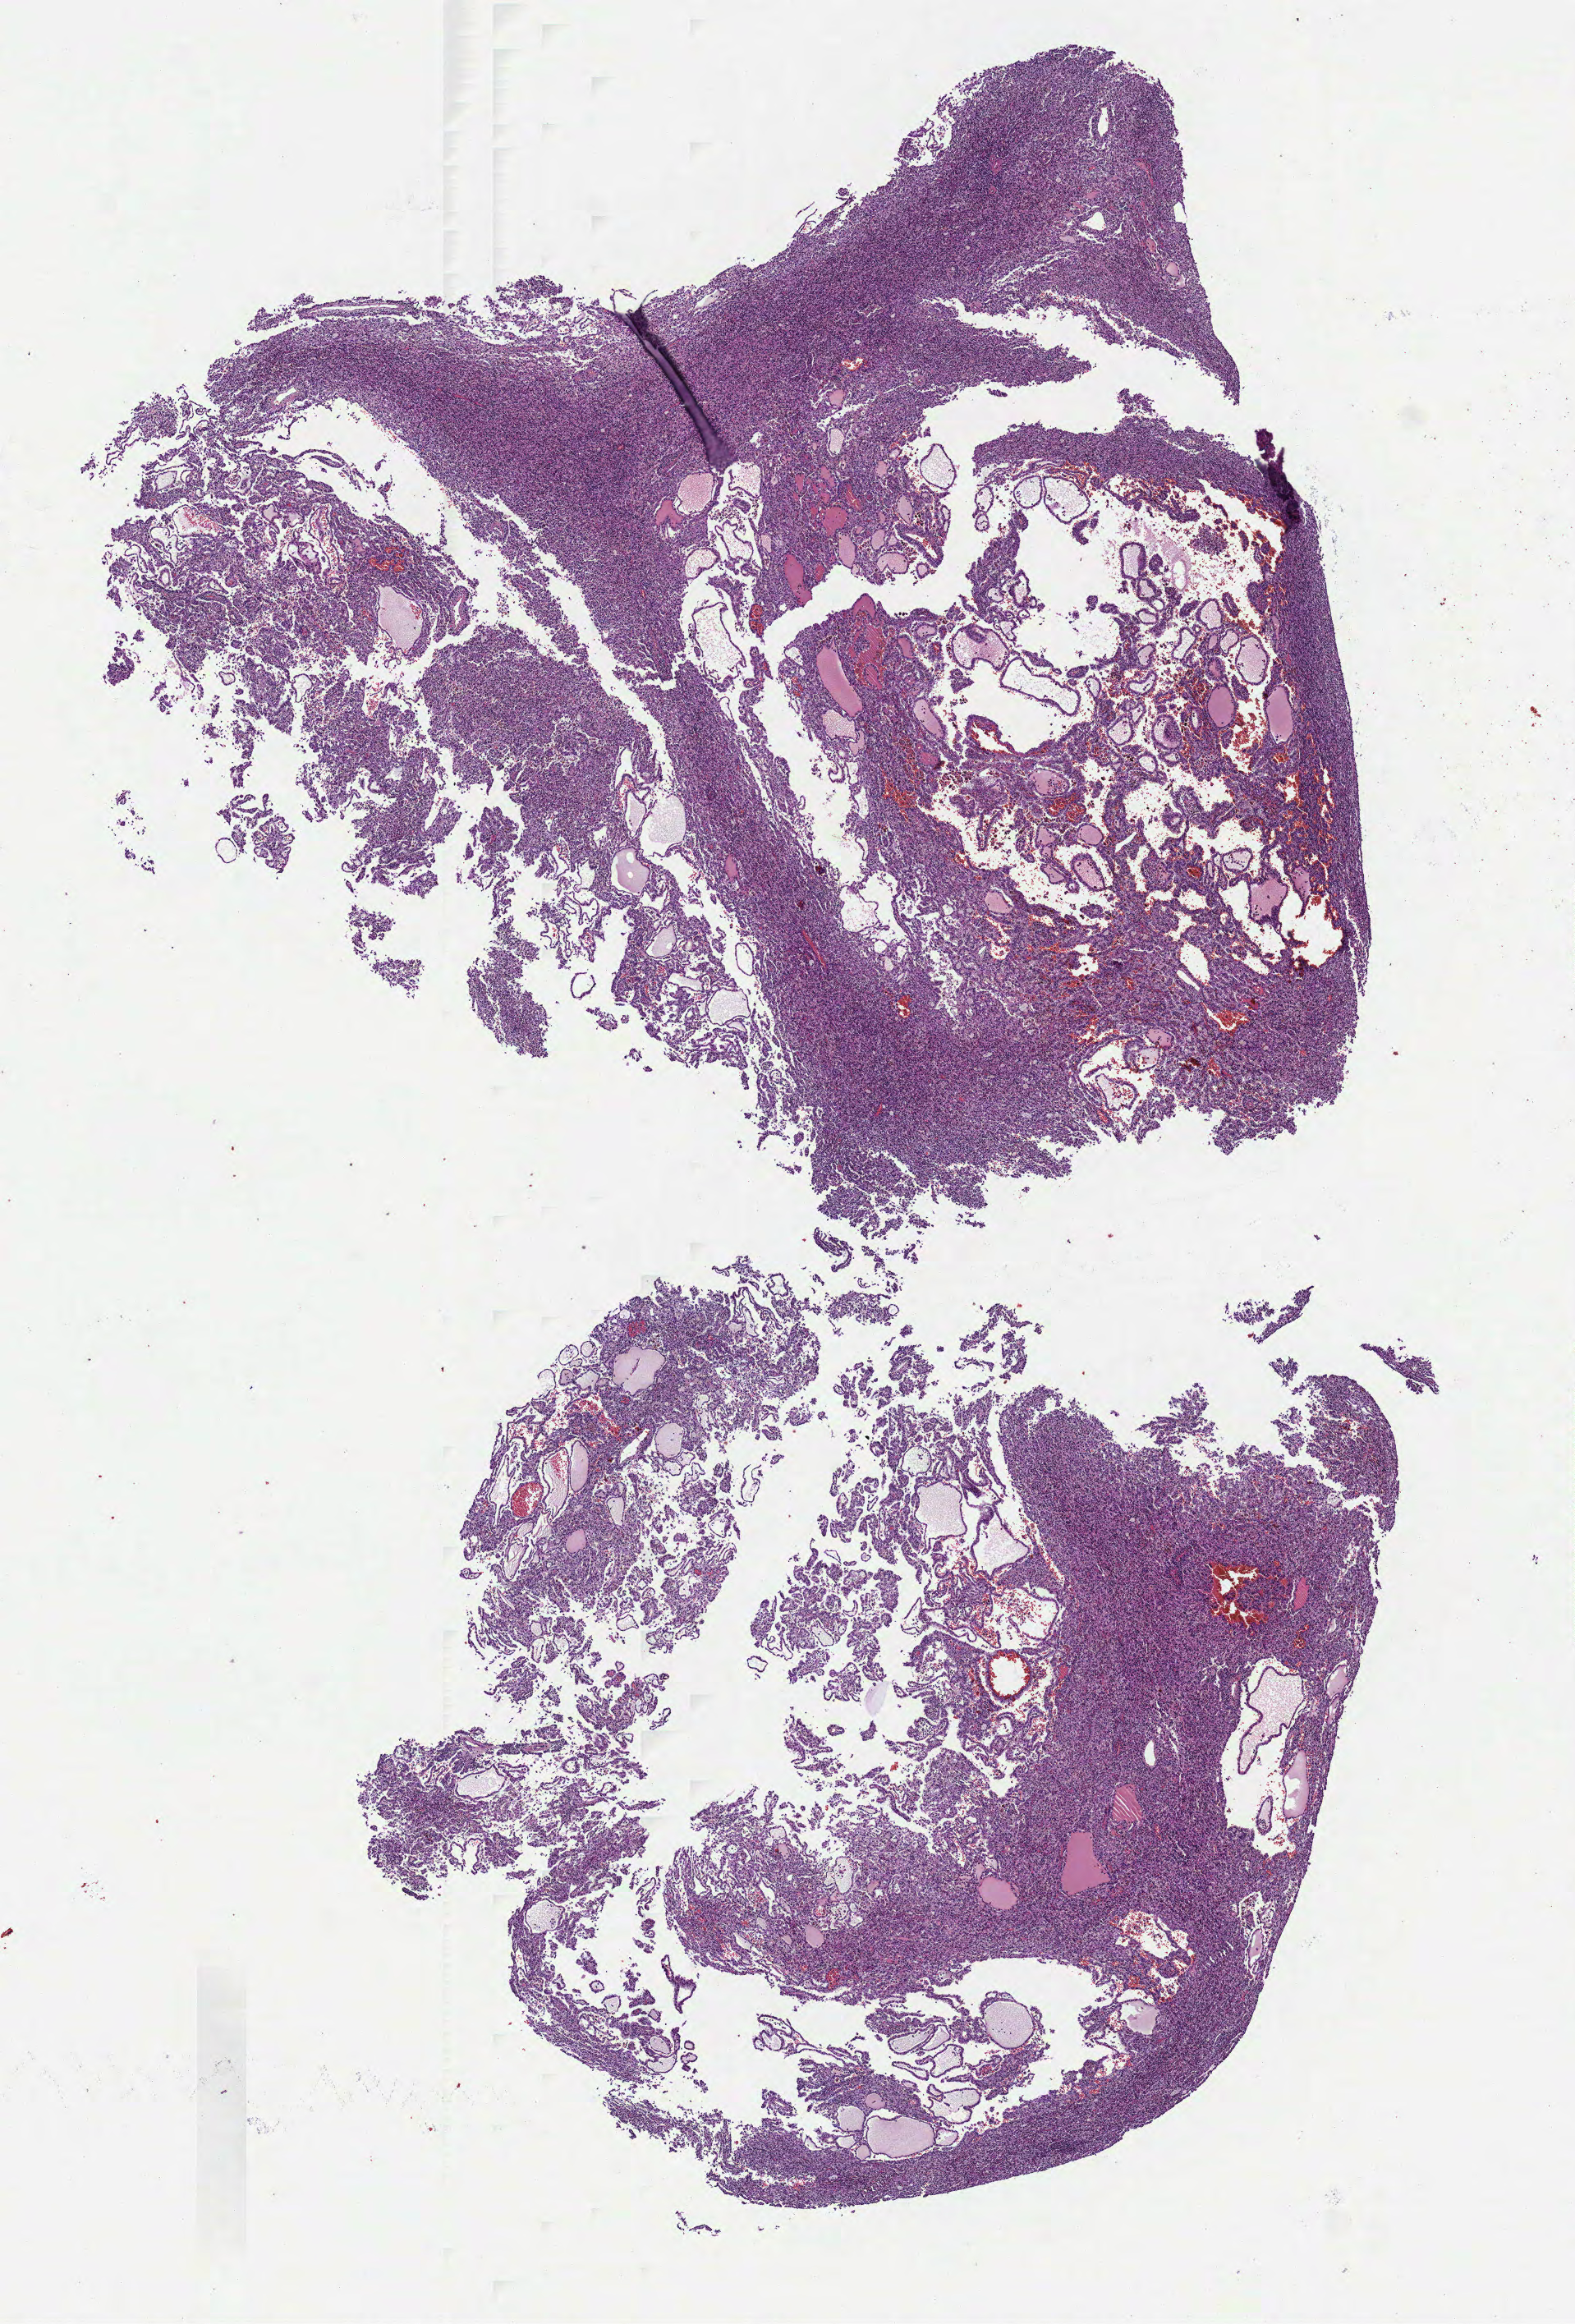
Digitized H&E-stained tissue section (whole slide) — a low-resolution overview of the entire scanned area, about 7.7 x 11.4 mm; formalin-fixed paraffin-embedded (FFPE) diagnostic section; primary tumour sample from the kidney. Patient: male, age at initial diagnosis 66 years.
Laterality: left. Diagnosis: Papillary adenocarcinoma, NOS. AJCC pathologic stage: I (7th edition).